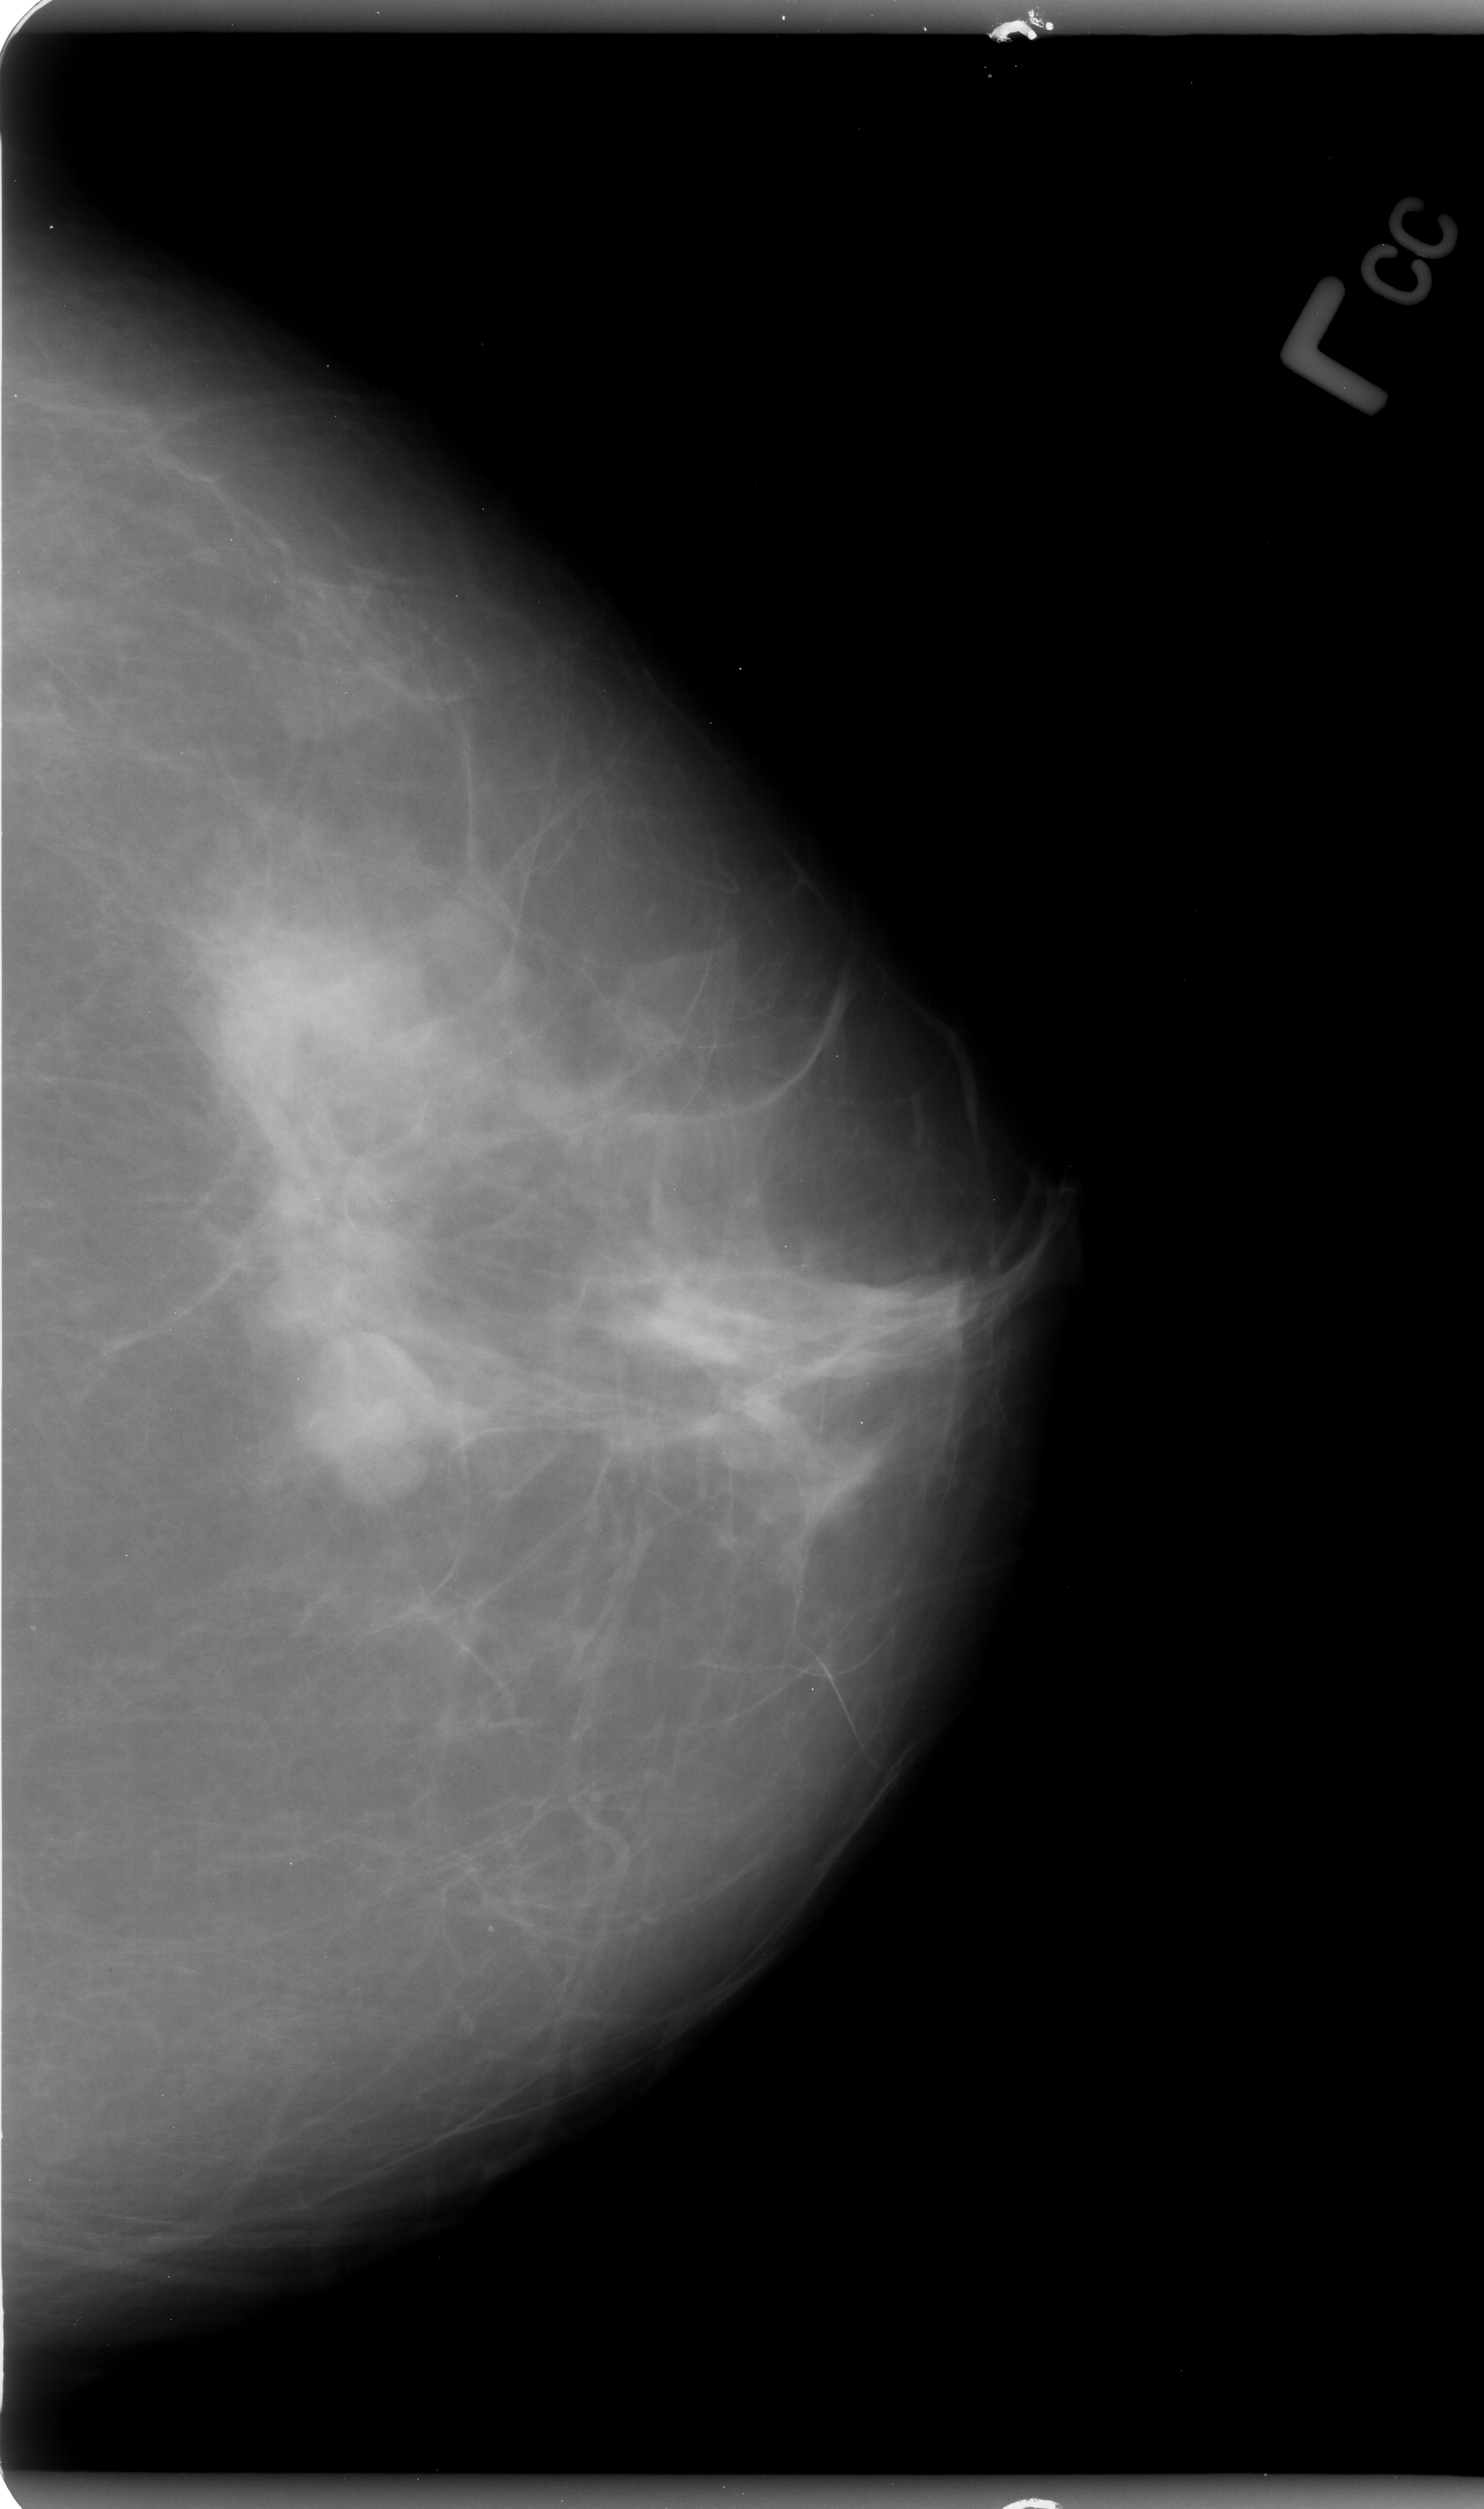
Scanned film-screen mammogram. Left breast. Craniocaudal (CC) view. Breast composition: scattered fibroglandular densities (BI-RADS density category 2 of 4). 1484 × 2509 image matrix.
Marked abnormalities (boxes around the expert regions of interest):
- mass, shape lobulated, margins circumscribed; BI-RADS assessment category 4; subtlety rating 3 on a 1 (subtle) to 5 (obvious) scale; pathology (as recorded): benign: bounding box <296,1355,435,1497> (left, top, right, bottom; pixels)